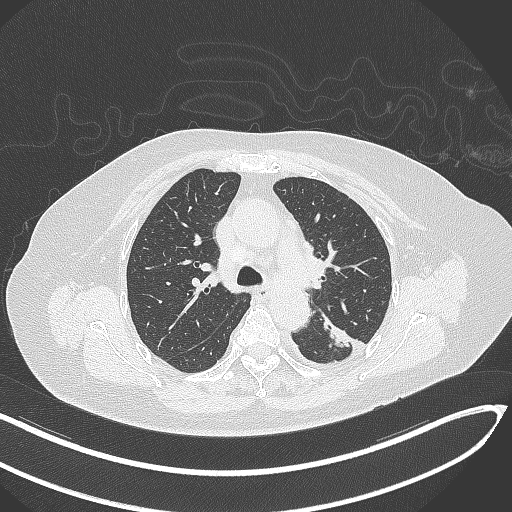
Chest CT, one axial slice. Slice 214 of 270 in the series (ordered by position). Lung window (W 1500 / L -600 HU). 1 mm slice thickness. 512 × 512 image matrix, field of view 400 × 400 mm. Patient: female, 76 years. From the clinical record (not read from this slice): clinical TNM (as recorded): T1c N0 M0.
Outlined on this slice (rectangle marked by the reading radiologist):
- lung tumour (recorded histology: adenocarcinoma): bounding box [x1, y1, x2, y2] px = [319, 312, 355, 353]